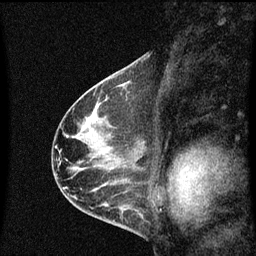
Breast MRI (dynamic contrast-enhanced), one sagittal slice; position 39 of 60 along the scan axis; dynamic contrast-enhanced series, image 2 of 3 at this slice position (ordered by acquisition); 1.5 T; TE 4.2 ms, TR 8.4 ms; 2 mm slice thickness; 256 × 256 image matrix, field of view 200 × 200 mm. Female patient, age 41 years.
Annotated regions visible in this slice (semi-automatically segmented with operator editing):
- analysis volume of interest (the breast-tissue region the enhancement analysis was run in; not a lesion): bounding box <121,74,145,99> (left, top, right, bottom; pixels)
- tumour enhancement mask (voxels above the 70 % enhancement threshold inside the analysis volume of interest): <126,86,130,93>